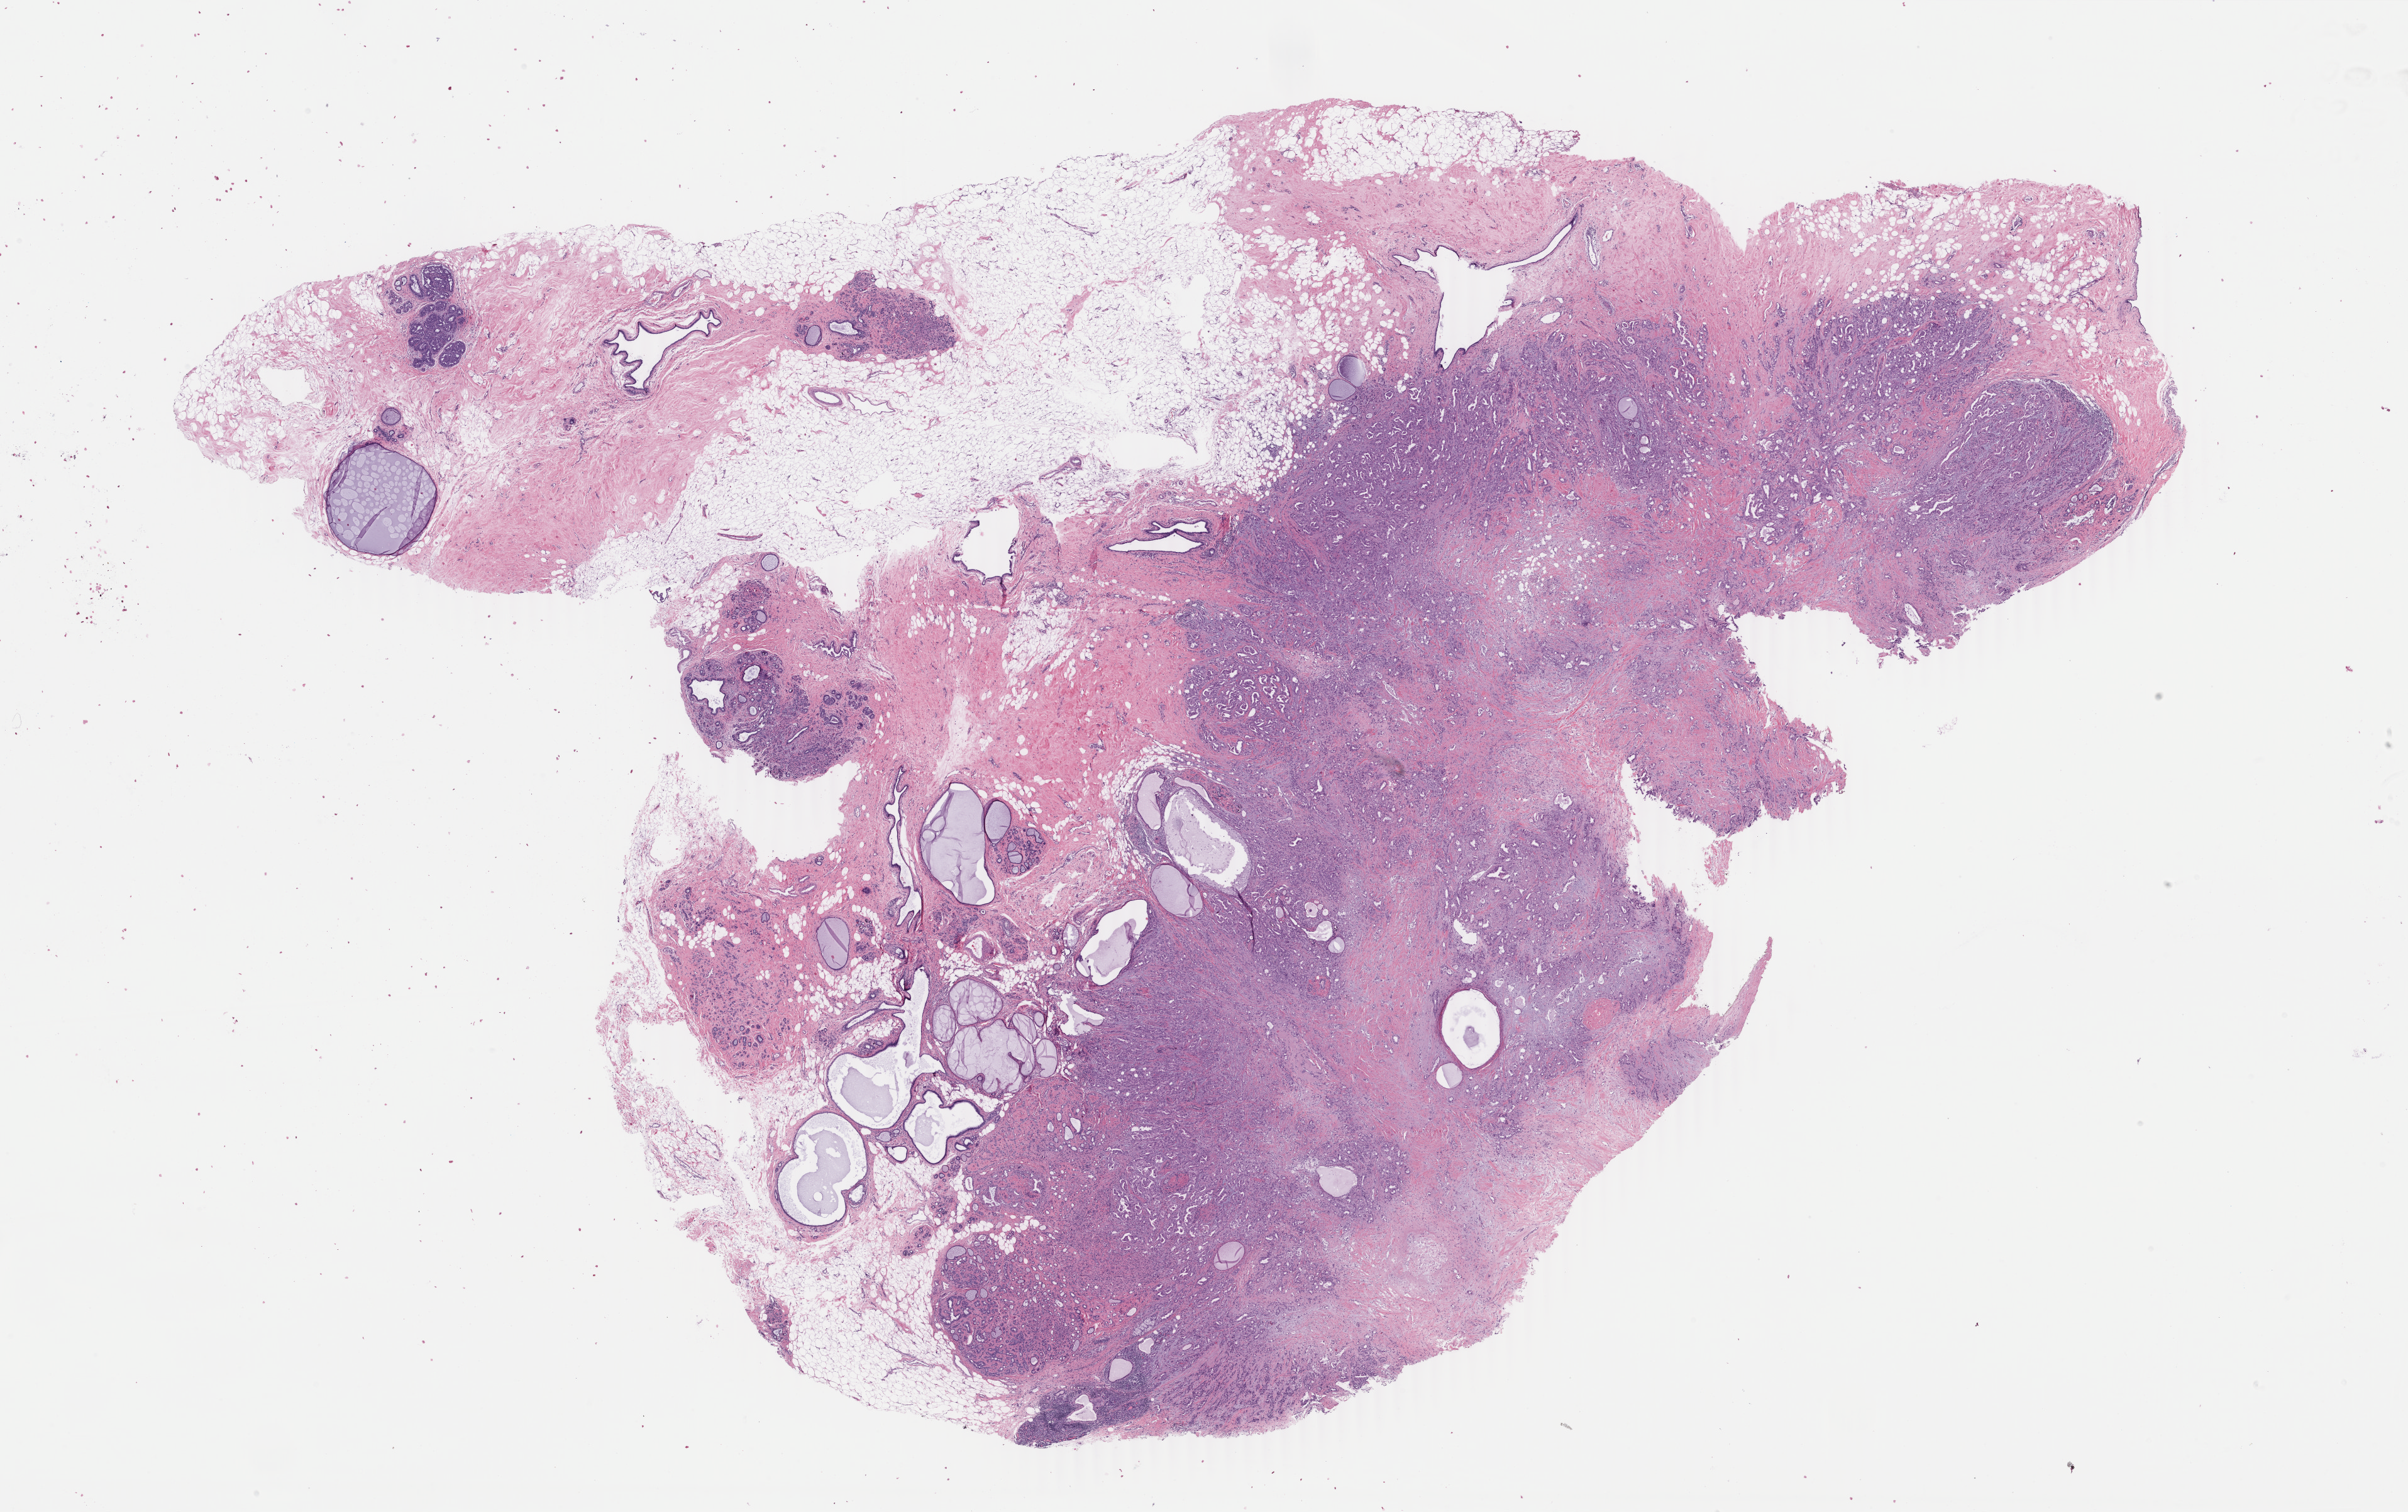
Whole-slide histology image, Hematoxylin and eosin (H&E) stained — whole scanned area (about 30.5 x 19.1 mm) shown as a low-resolution overview; FFPE section; primary tumour sample from the breast. Female, age 50 years at initial diagnosis.
* histologic diagnosis: Infiltrating duct carcinoma, NOS
* TNM: T2 N2a M0
* AJCC pathologic stage: IIIA (7th edition)